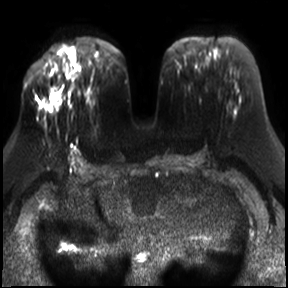
Breast MRI, one axial slice. Position 13 of 30 along the scan axis. Diffusion-weighted series; image 2 of 4 stored at this slice position (different b-values; order by instance number). 3 T. 4 mm slice thickness. 288 × 288 image matrix. Female patient.
Structures marked on this image (expert manual segmentation):
- tumour on diffusion-weighted imaging: bounding box <53,93,56,96> (left, top, right, bottom; pixels)